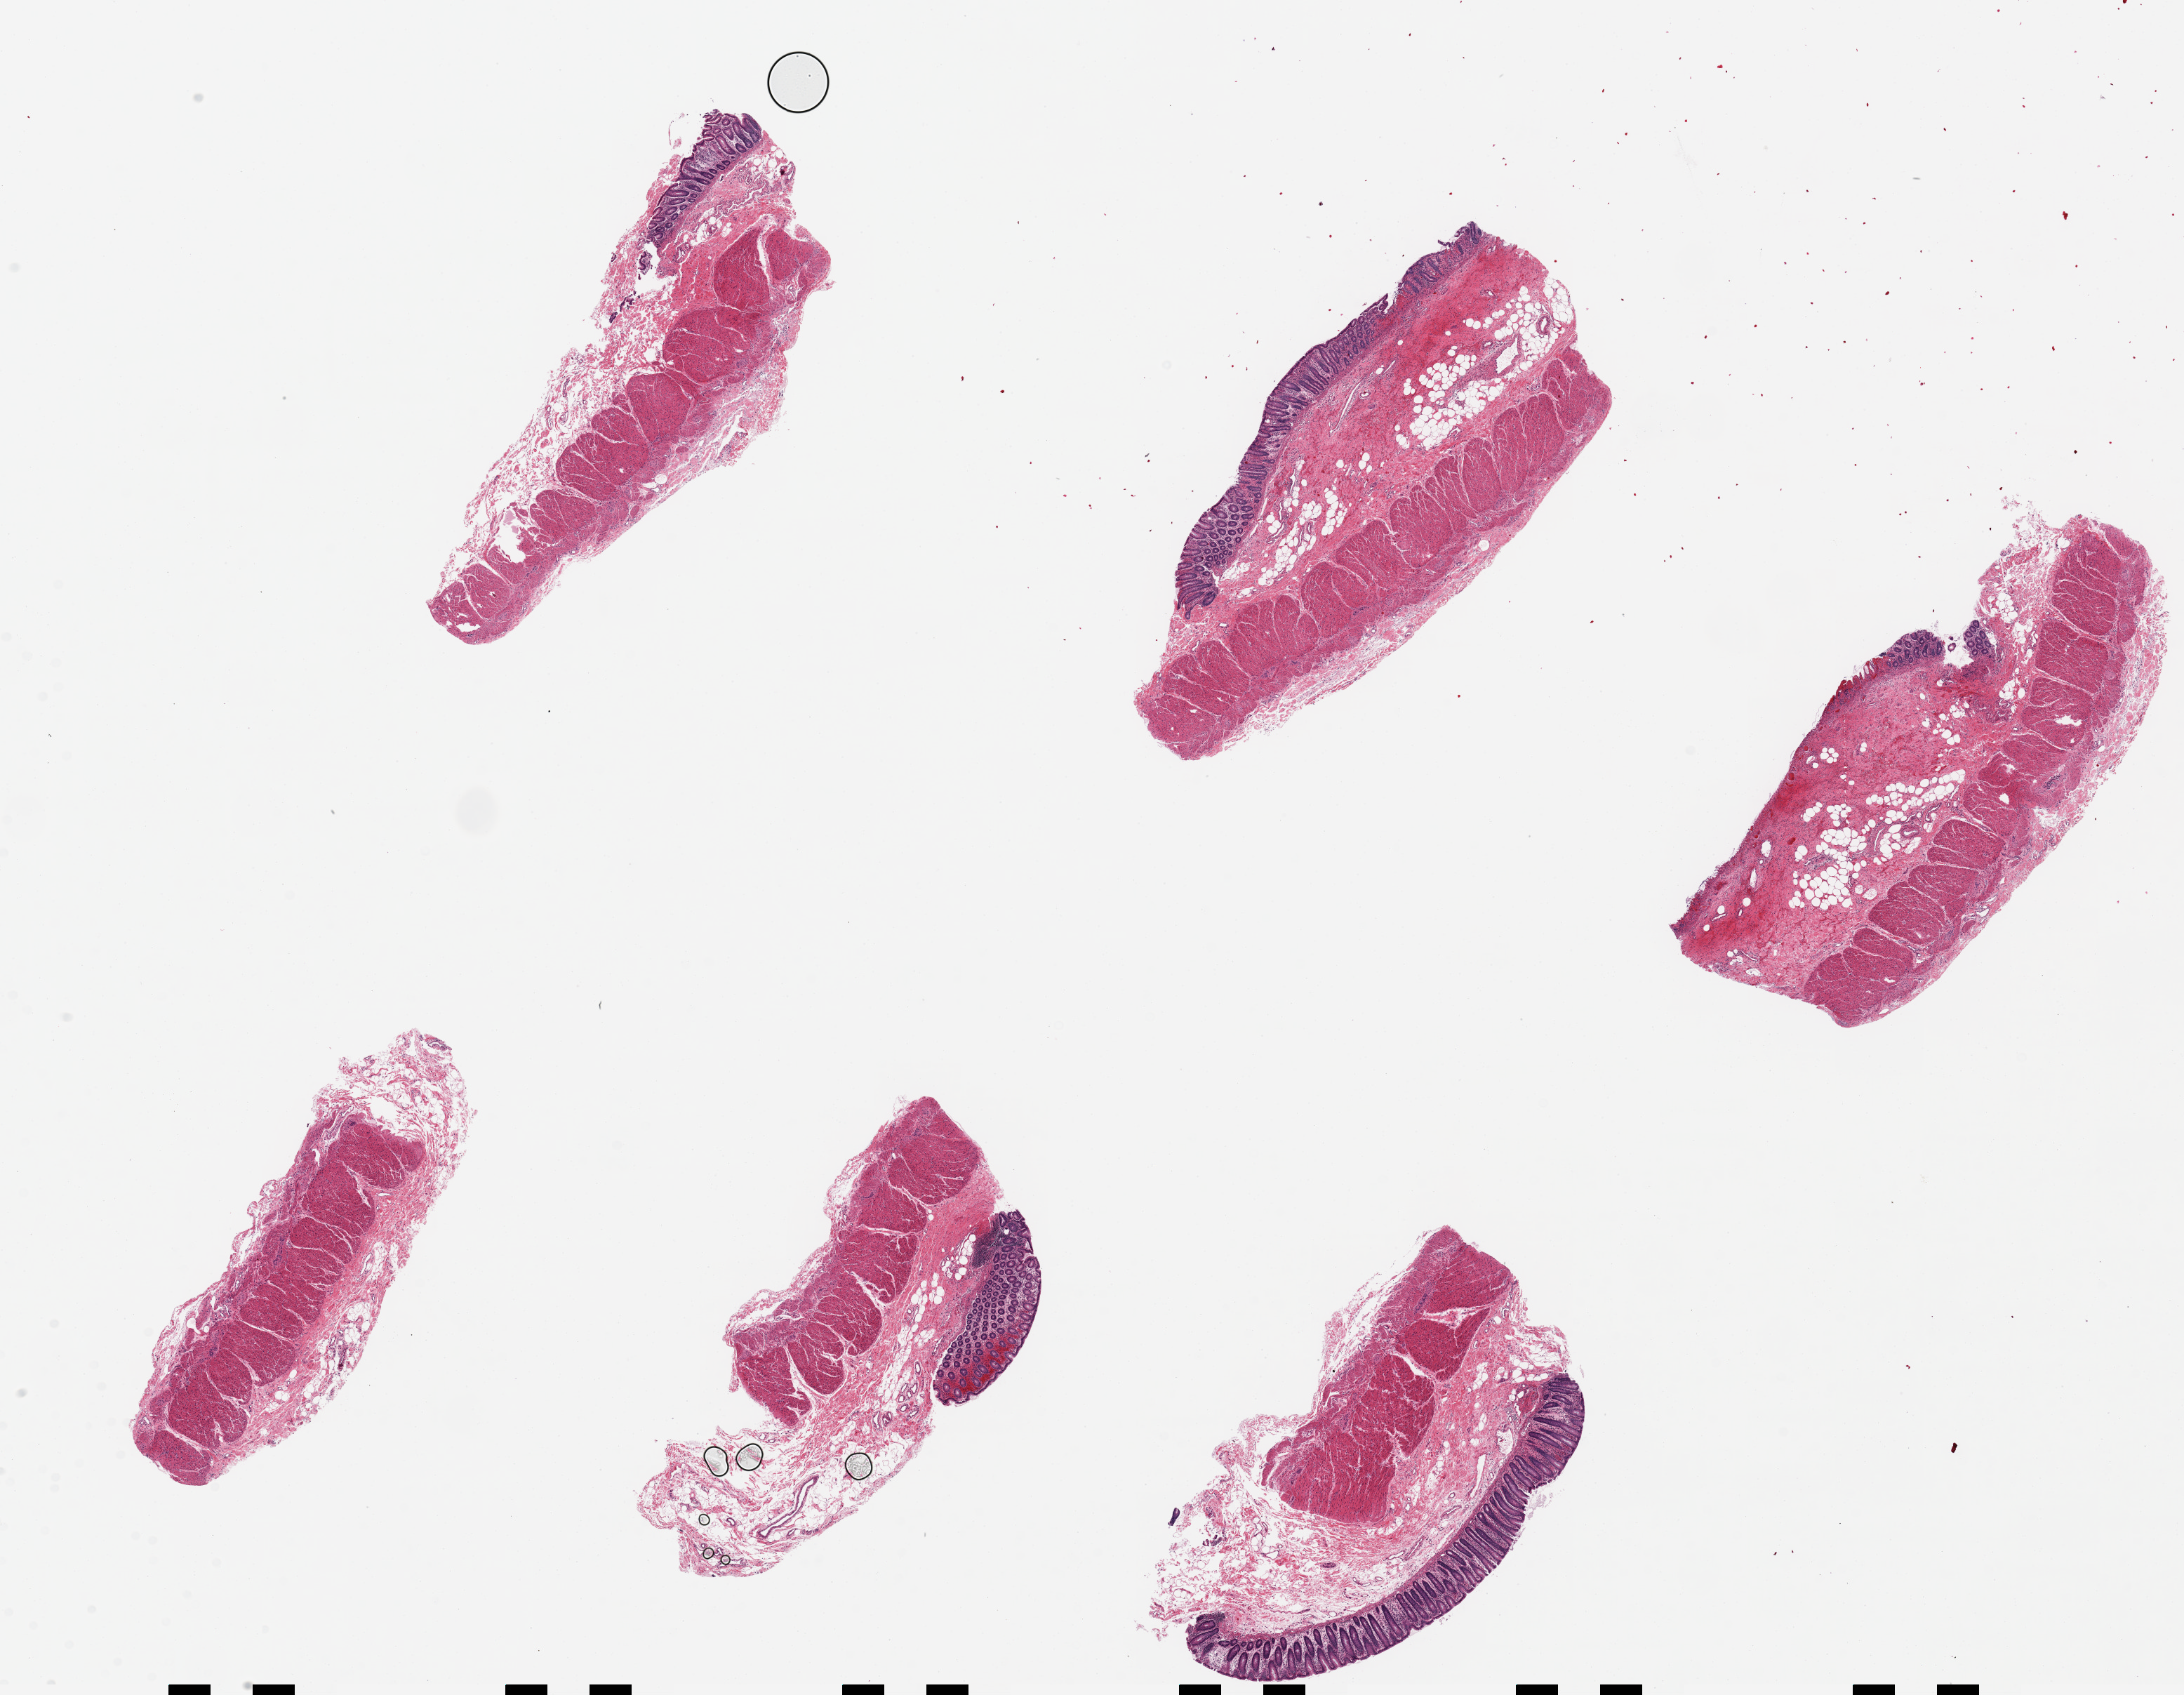
Haematoxylin and eosin whole-slide image — shown as a low-resolution overview of the whole scanned area (about 24.6 x 19.1 mm, acquisition: 20x scan); PAXgene-fixed paraffin-embedded (PFPE) section; section of transverse colon (target tissue); tissue donor sample. Male donor.
- pathologist's review note for this sample: 6 pieces ~7x3mm; mucosa well preserved but less than 10% total tissue, some aliquots have none